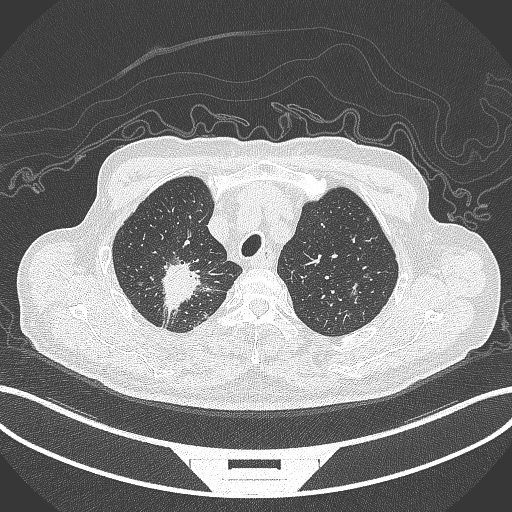
Chest CT, one axial slice; position 314 of 407 along the scan axis; reconstruction kernel B70f; 120 kVp; lung window (W 1500 / L -600 HU); 1 mm slice thickness; 512 × 512 image matrix. Male patient, age 69 years. From the clinical record (not read from this slice): clinical TNM (as recorded): T1c N1 M1.
Annotated regions visible in this slice (bounding box drawn by a radiologist):
- lung tumour (recorded histology: adenocarcinoma): box from (x=156, y=256) to (x=209, y=316) px